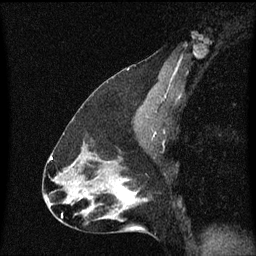
Breast MRI (dynamic contrast-enhanced), one sagittal slice; position 37 of 60 along the scan axis; dynamic contrast-enhanced series, image 2 of 3 at this slice position (ordered by acquisition); 1.5 T; TE 4.2 ms, TR 8.4 ms; 2 mm slice thickness; 256 × 256 image matrix, field of view 200 × 200 mm. Female patient, age 47 years.
Outlined on this slice (semi-automatically segmented with operator editing):
- analysis volume of interest (the breast-tissue region the enhancement analysis was run in; not a lesion): bounding box <100,172,149,219> (left, top, right, bottom; pixels)
- tumour enhancement mask (voxels above the 70 % enhancement threshold inside the analysis volume of interest): <118,184,135,211>